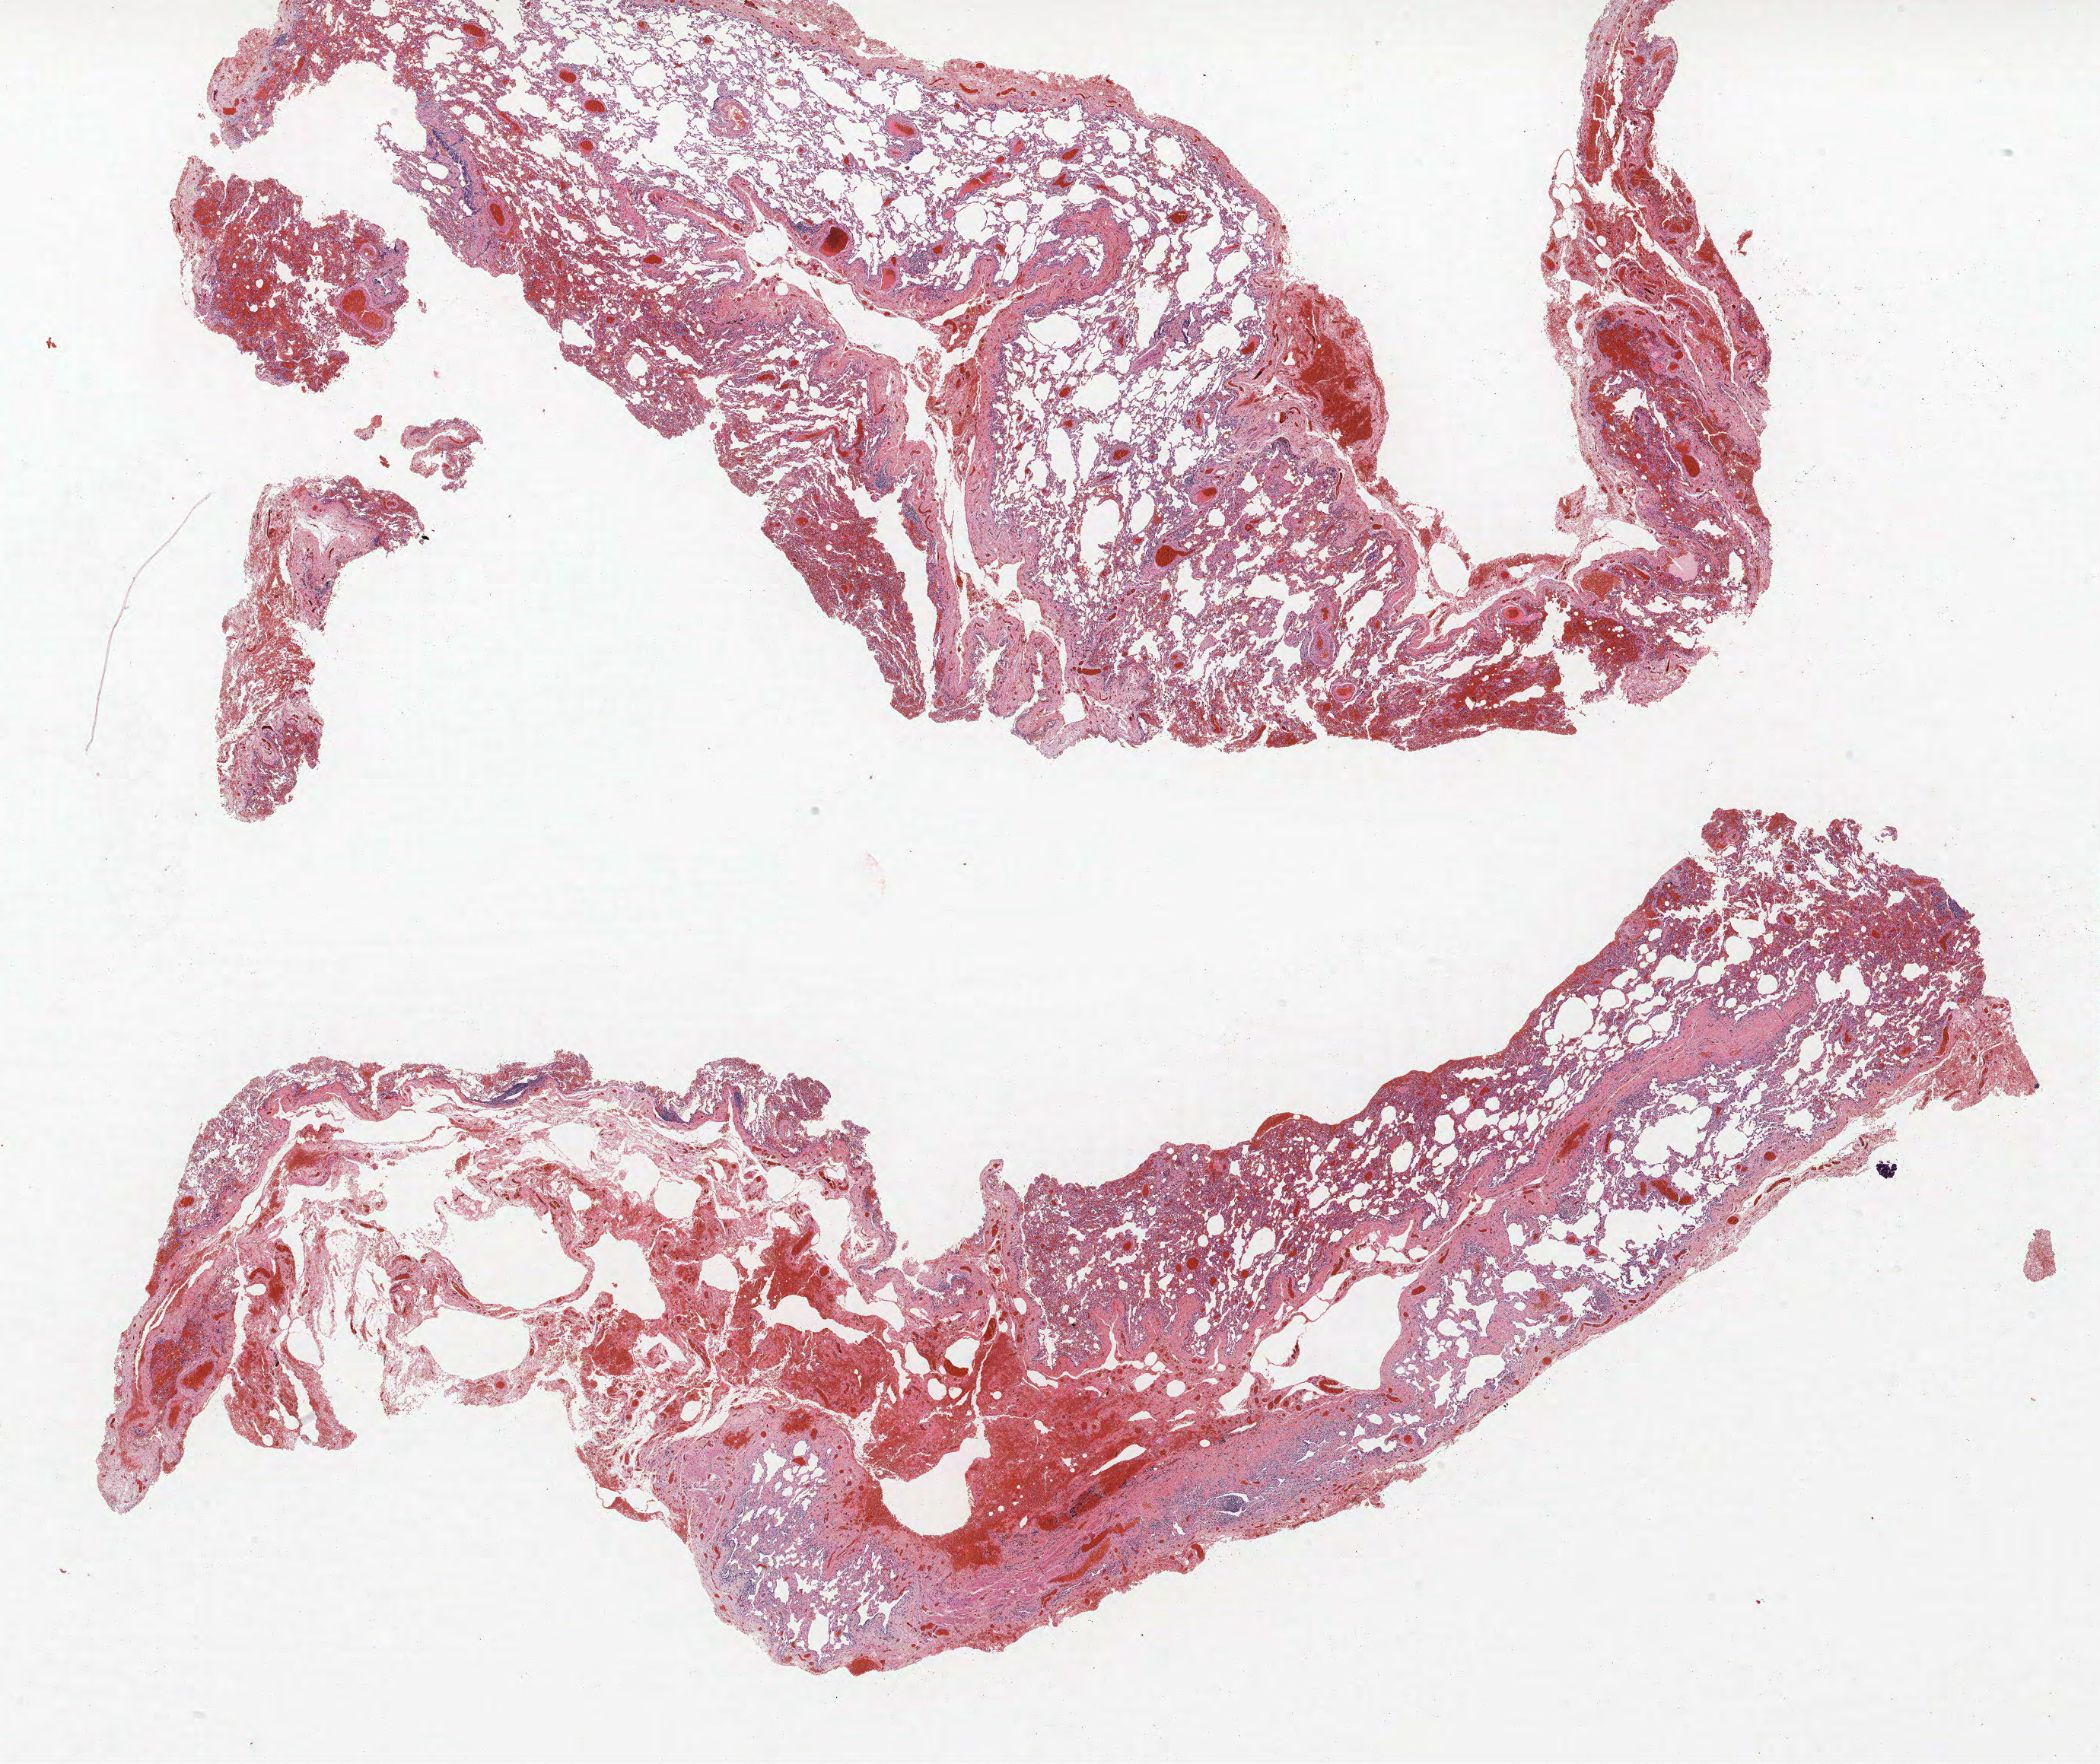
Hematoxylin and eosin (H&E) stained whole-slide image, shown as a low-resolution overview of the whole scanned area (about 22.1 x 18.6 mm); formalin-fixed paraffin-embedded (FFPE) section; lung tissue. Male, age 68 at enrolment. Current smoker at enrolment. Grade: well differentiated (G1).
• tumour size (pathology): 12 mm
• primary tumour location (clinical record): right lower lobe
• stage (AJCC 6th edition): IA
• participant's lung-cancer diagnosis: Bronchiolo-alveolar adenocarcinoma, NOS